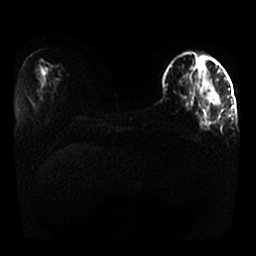
Breast MRI, one axial slice. Slice 11 of 25 in the series (ordered by position). Diffusion-weighted series; image 2 of 4 stored at this slice position (different b-values; order by instance number). 1.5 T. 256 × 256 image matrix. Female patient.
Outlined on this slice (manually delineated by an expert):
- tumour on diffusion-weighted imaging: bounding box (x1, y1, x2, y2) in pixels: (206, 91, 219, 105)